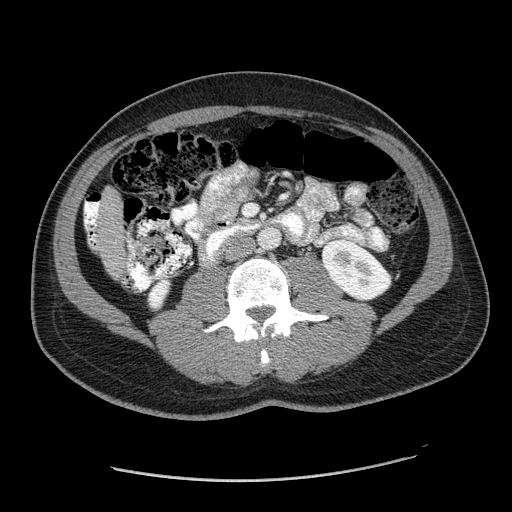
Contrast-enhanced abdominal CT (liver protocol), one axial slice. Position 31 of 182 along the scan axis. Soft-tissue window (W 400 / L 40 HU). 2.5 mm slice thickness. 512 × 512 image matrix. From the clinical record (not read from this slice): diagnosis: hepatocellular carcinoma (patient treated with transarterial chemoembolisation; whether this scan precedes or follows treatment is not stated here); TNM stage (as recorded): Stage-I; Child-Pugh class: A; tumour differentiation: well differentiated; tumour nodularity: uninodular.
Outlined on this slice (semi-automatic segmentation, software-assisted and operator-edited):
- liver parenchyma outside the tumour (the mass and vessels are separate outlines, so this box may not span the whole liver): box from (x=84, y=186) to (x=126, y=276) px
- liver vessels: (x=84, y=202)–(x=99, y=225)